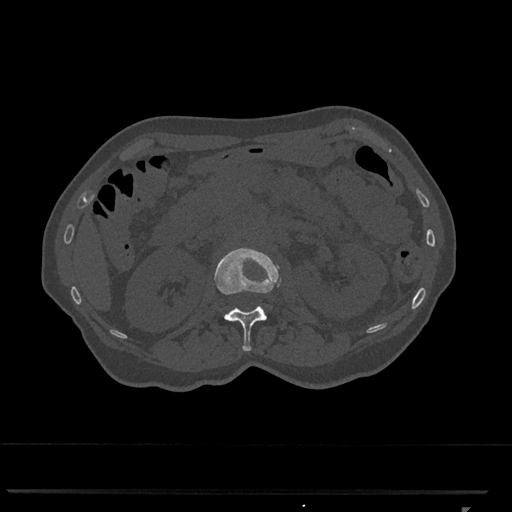
CT including the spine, one axial slice. Slice 389 of 793 in the series (ordered by position). Bone window (W 1800 / L 400 HU). 512 × 512 image matrix, field of view 380 × 380 mm. Patient: female, 62 years. Case-level facts recorded for this patient, not image findings: primary cancer: renal.
Annotated regions visible in this slice (semi-automatically segmented with operator editing):
- L1 vertebra: bounding box [x1, y1, x2, y2] px = [214, 248, 281, 351]
- L2 vertebra: [255, 250, 261, 253]